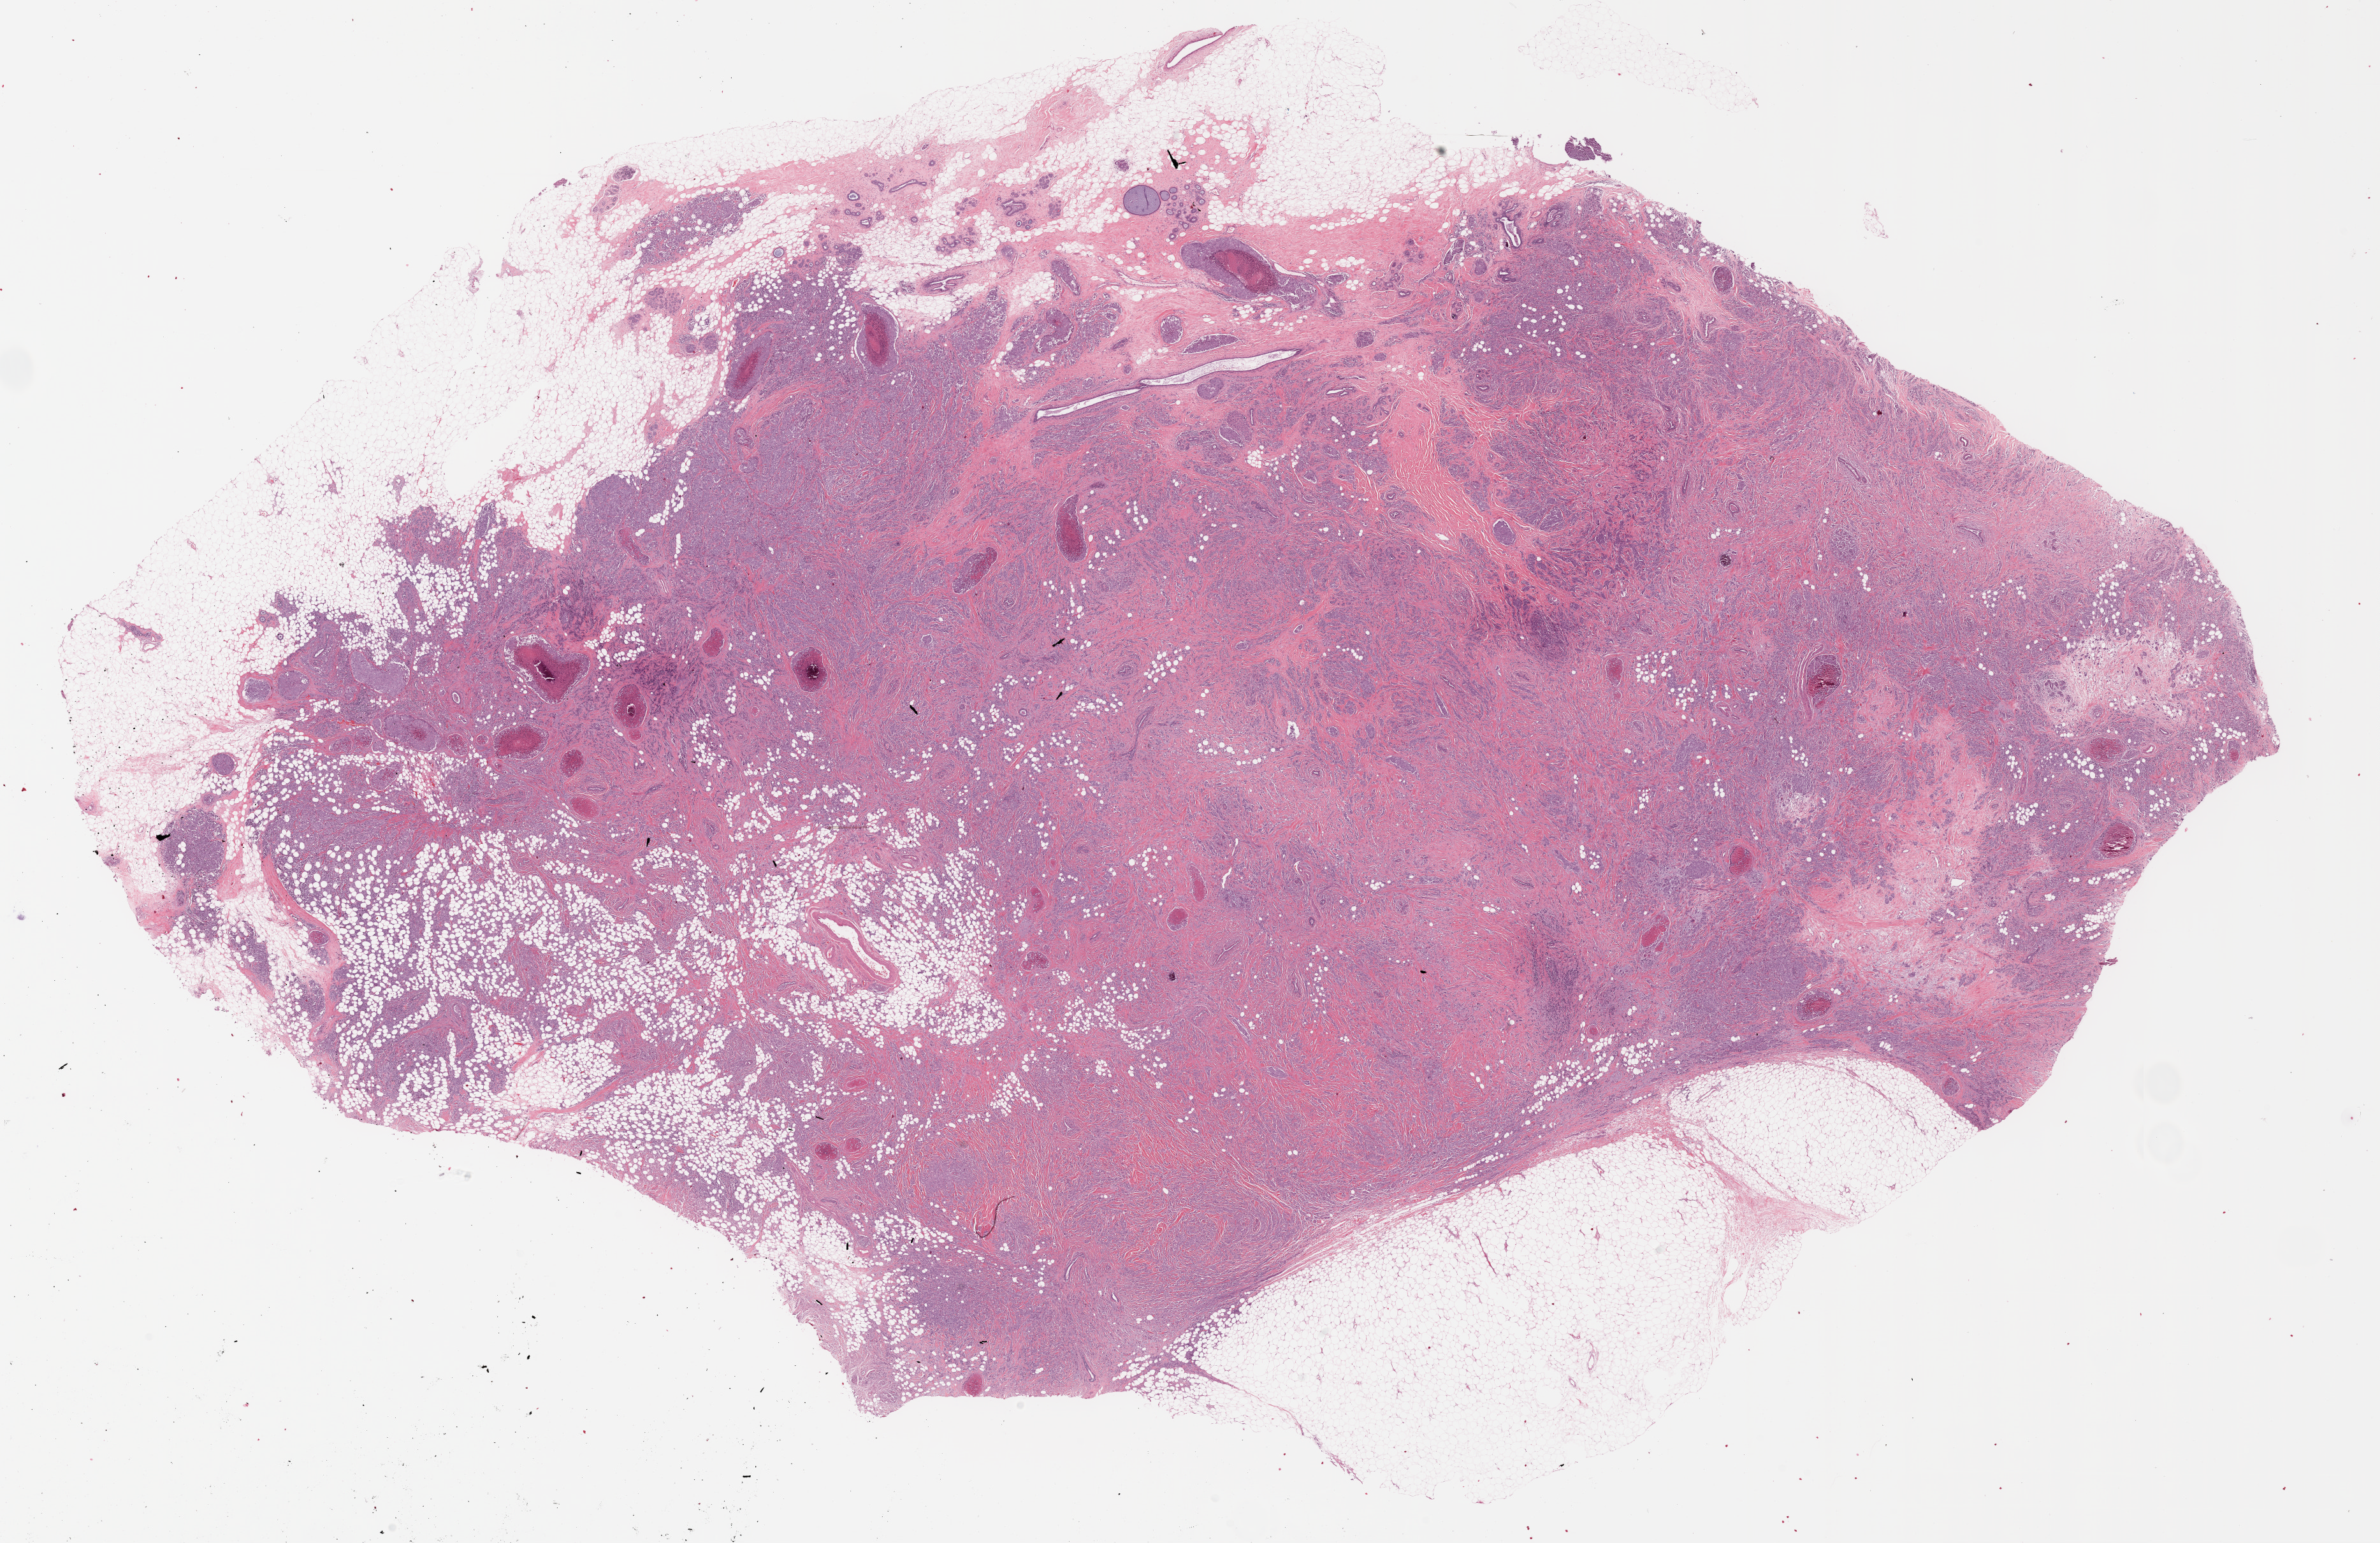
Digitized H&E-stained tissue section (whole slide) — shown as a low-resolution overview of the whole scanned area (about 29.8 x 19.3 mm), formalin-fixed paraffin-embedded (FFPE) diagnostic section, breast, primary tumour sample. Patient: female, age at initial diagnosis 50 years.
Lymph nodes positive (case pathology): 1 of 14 examined. Diagnosis: Infiltrating duct carcinoma, NOS. AJCC pathologic stage: IIIA.